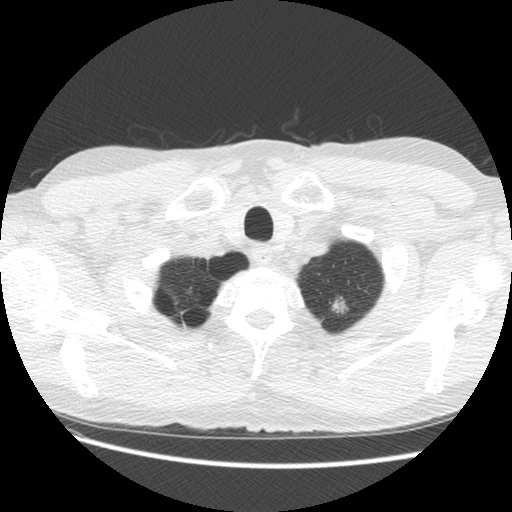
Low-dose screening chest CT, axial slice, second annual screen, lung window (W 1500 / L -600 HU), 2.5 mm slice thickness, 512 × 512 image matrix. Male, age 63 years at enrolment.
Expert-annotated lung lesion, box from (x=316, y=285) to (x=366, y=326) px. The screening reader recorded 2 non-calcified nodules or masses ≥4 mm on this exam (left upper lobe, right lower lobe); which of them this box marks is not recorded.